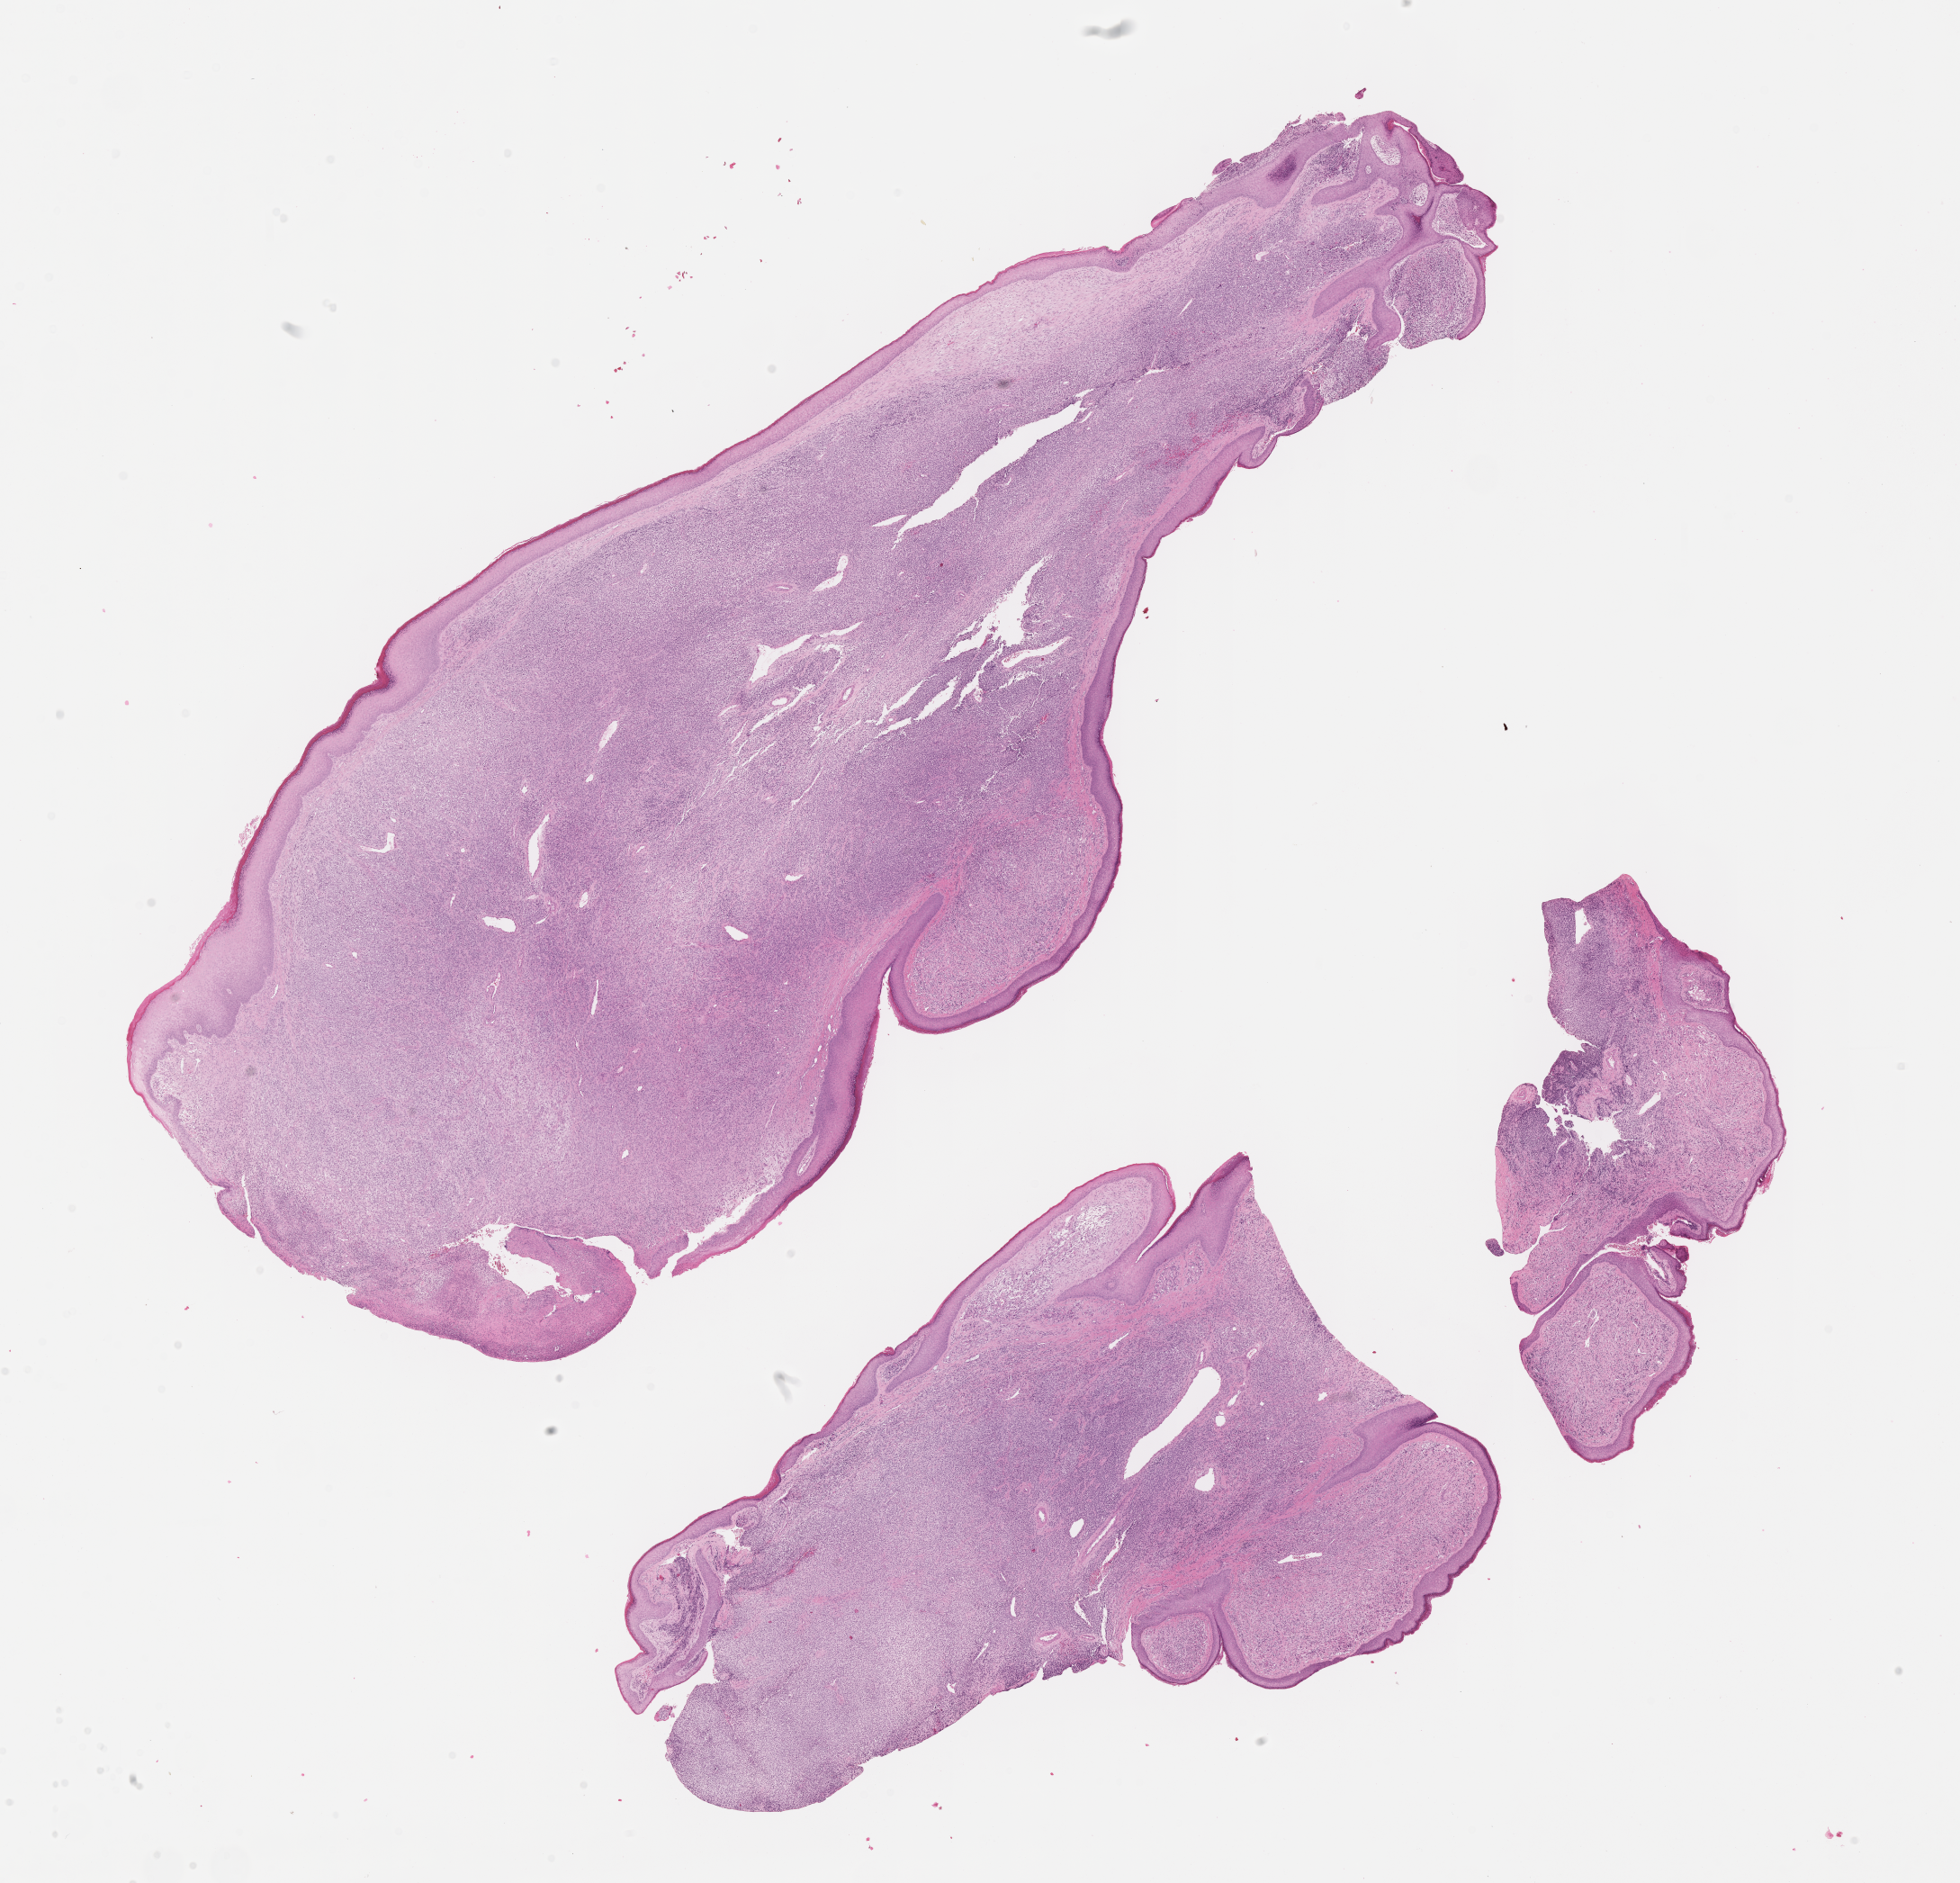
Hematoxylin and eosin (H&E) whole-slide image of tumor tissue — shown as a low-resolution overview of the whole scanned area (about 17.6 x 16.9 mm). FFPE section. Sample anatomic site: soft tissue, ear-right. Patient: female, age 2.5 years at diagnosis.
* stage (as recorded): 3
* diagnosis: rhabdomyosarcoma; histological classification: embryonal rhabdomyosarcoma